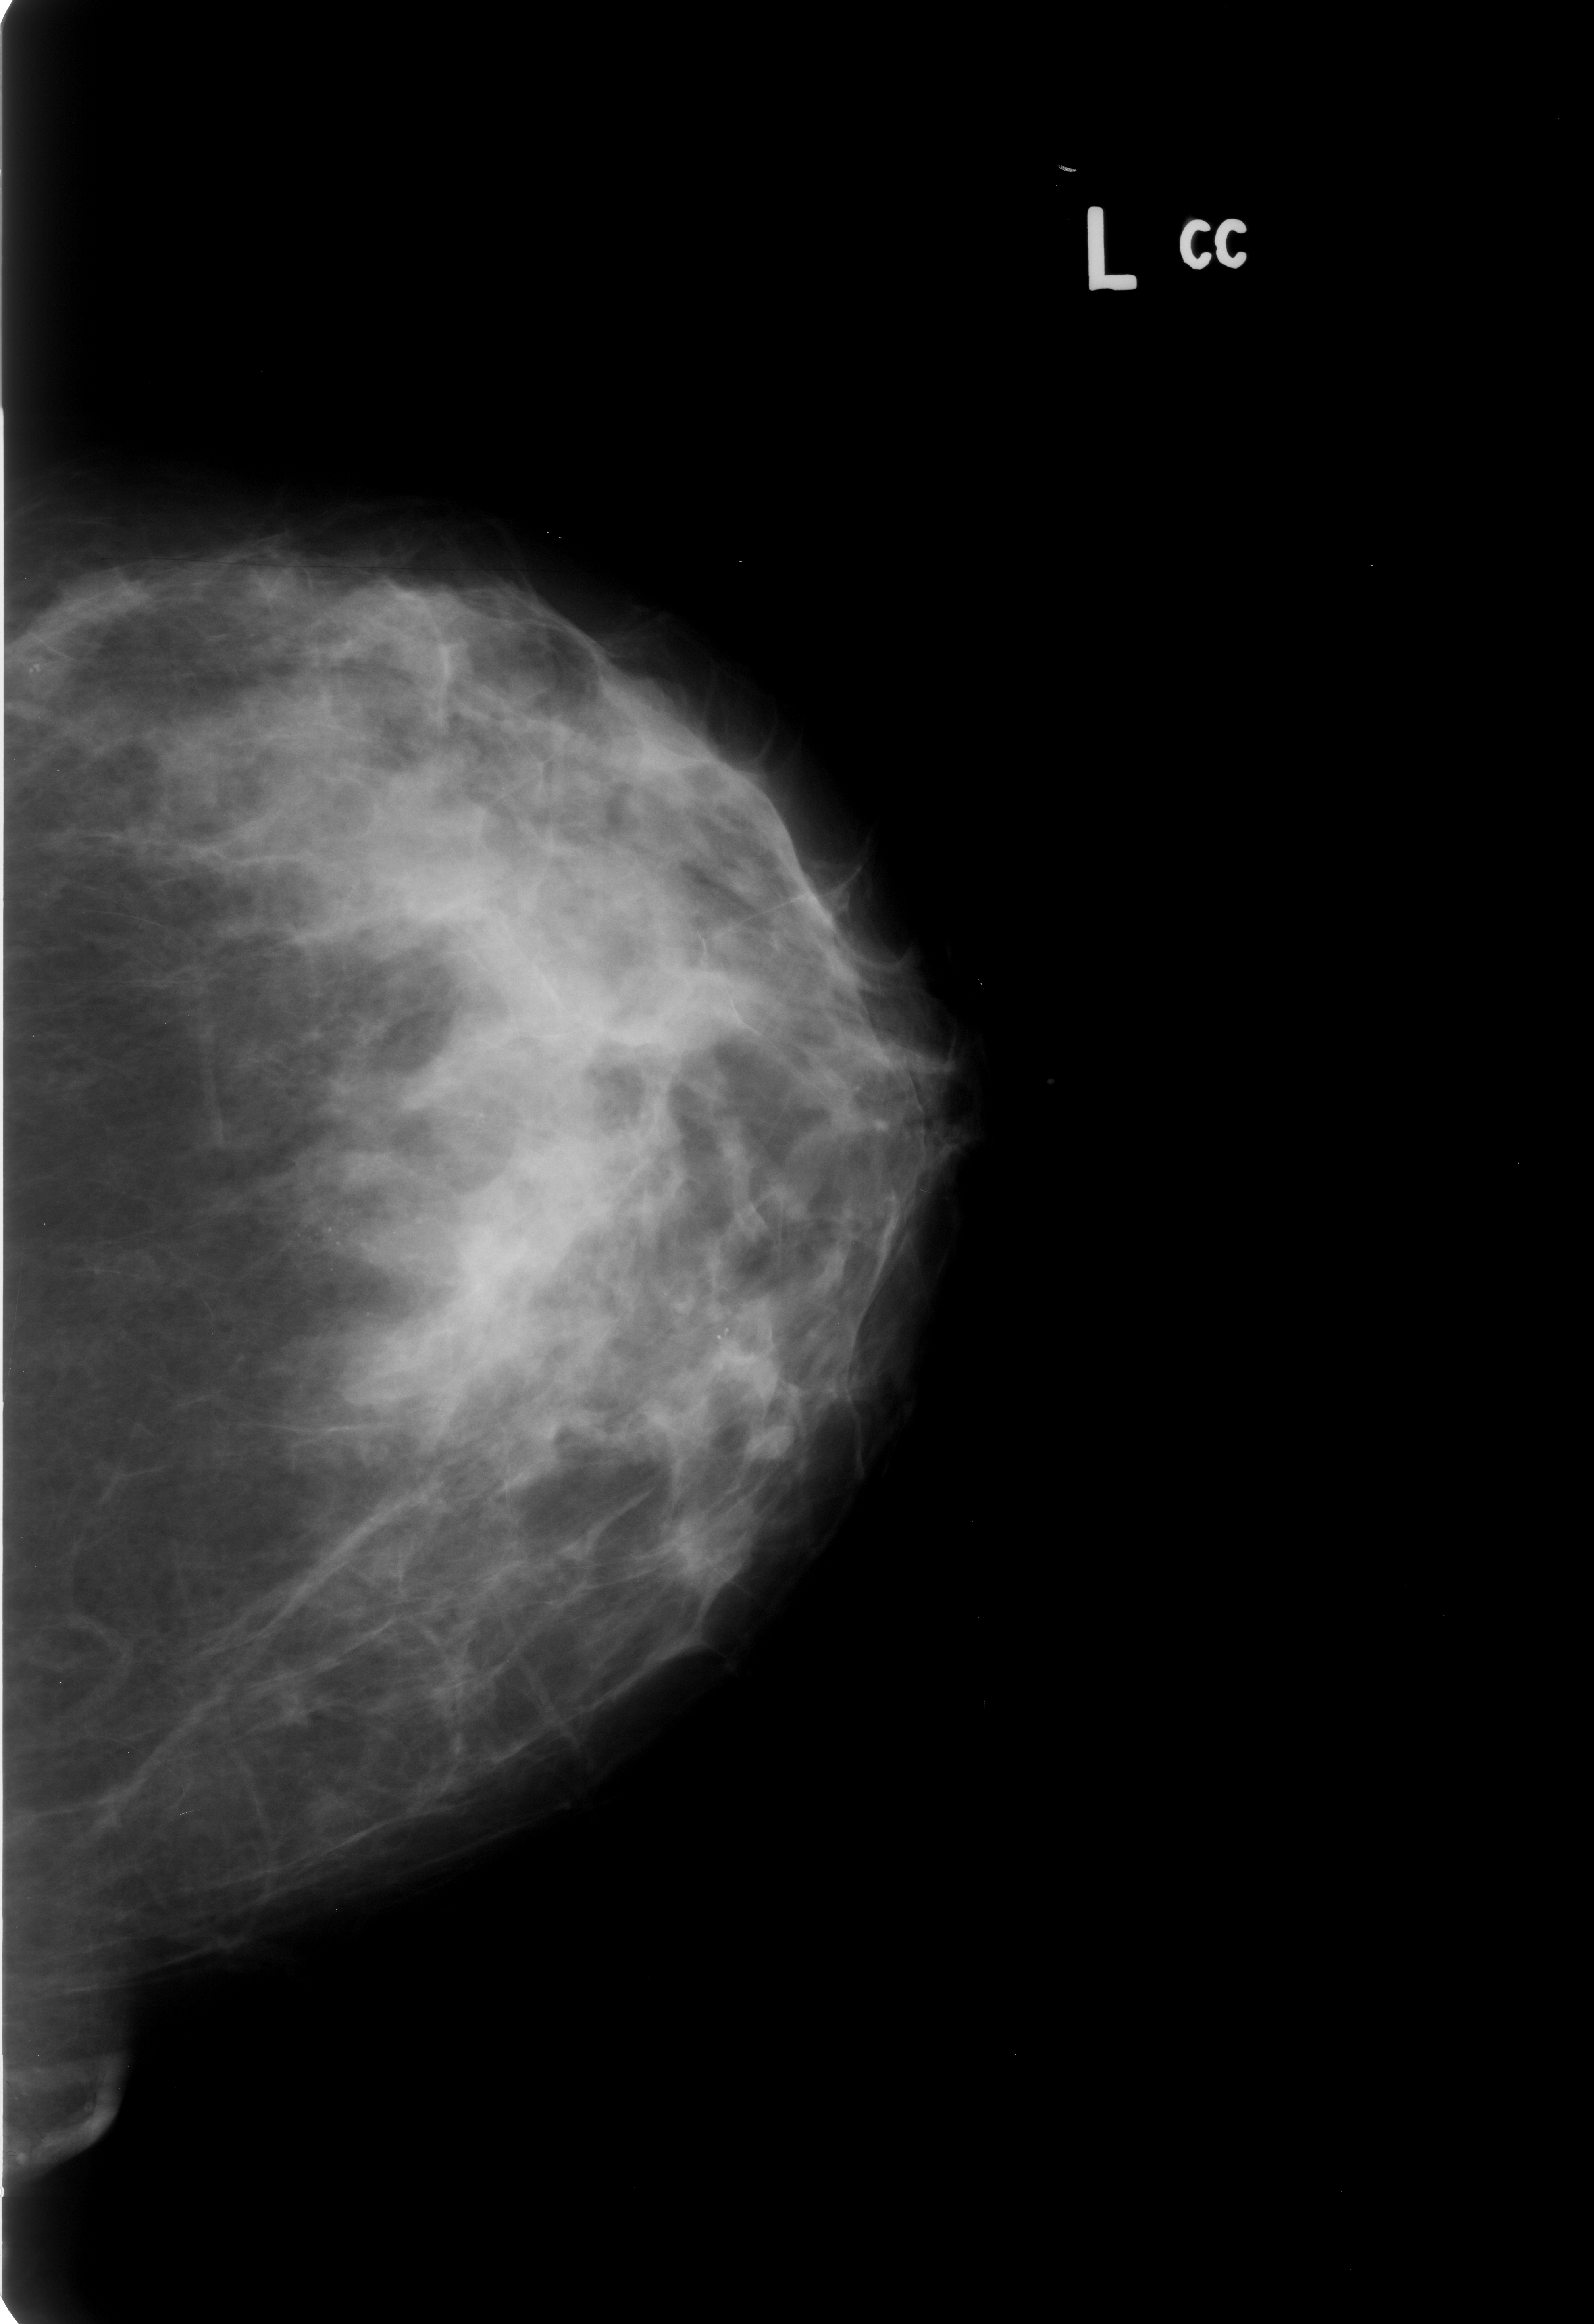
Scanned film-screen mammogram; left breast; CC view; breast composition: heterogeneously dense (BI-RADS density category 3 of 4).
Abnormality record for this image: Finding 1 of 2: calcifications, morphology pleomorphic, distribution segmental; BI-RADS assessment category 4; subtlety rating 3 on a 1 (subtle) to 5 (obvious) scale; pathology result (as recorded, not read from the image): benign. Finding 2 of 2: calcifications, morphology pleomorphic, distribution segmental; BI-RADS assessment category 4; pathology result (as recorded, not read from the image): benign.